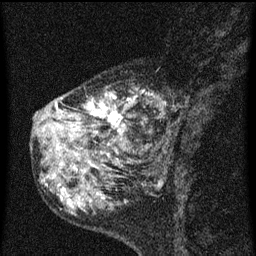
Breast MRI (dynamic contrast-enhanced), one sagittal slice. Slice 22 of 60 in the series (ordered by position). Dynamic contrast-enhanced series, image 2 of 3 at this slice position (ordered by acquisition). 1.5 T. TE 4.2 ms, TR 8 ms. 2 mm slice thickness. 256 × 256 image matrix, field of view 180 × 180 mm. Female patient, age 55 years.
Outlined on this slice (semi-automatically segmented with operator editing):
- analysis volume of interest (the breast-tissue region the enhancement analysis was run in; not a lesion): bounding box [x1, y1, x2, y2] px = [42, 72, 182, 155]
- tumour enhancement mask (voxels above the 70 % enhancement threshold inside the analysis volume of interest): [56, 92, 167, 147]